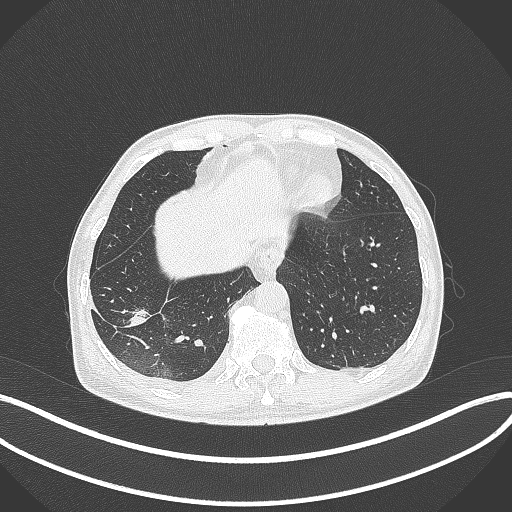
Chest CT, one axial slice. Position 82 of 388 along the scan axis. Reconstruction kernel B70f. Lung window (W 1500 / L -600 HU). 512 × 512 image matrix, field of view 400 × 400 mm. Male patient, age 64 years. Case-level facts recorded for this patient, not image findings: clinical TNM (as recorded): T3 N0 M0.
Annotated regions visible in this slice (rectangle marked by the reading radiologist):
- lung tumour (recorded histology: adenocarcinoma): bounding box (x1, y1, x2, y2) in pixels: (119, 307, 152, 330)